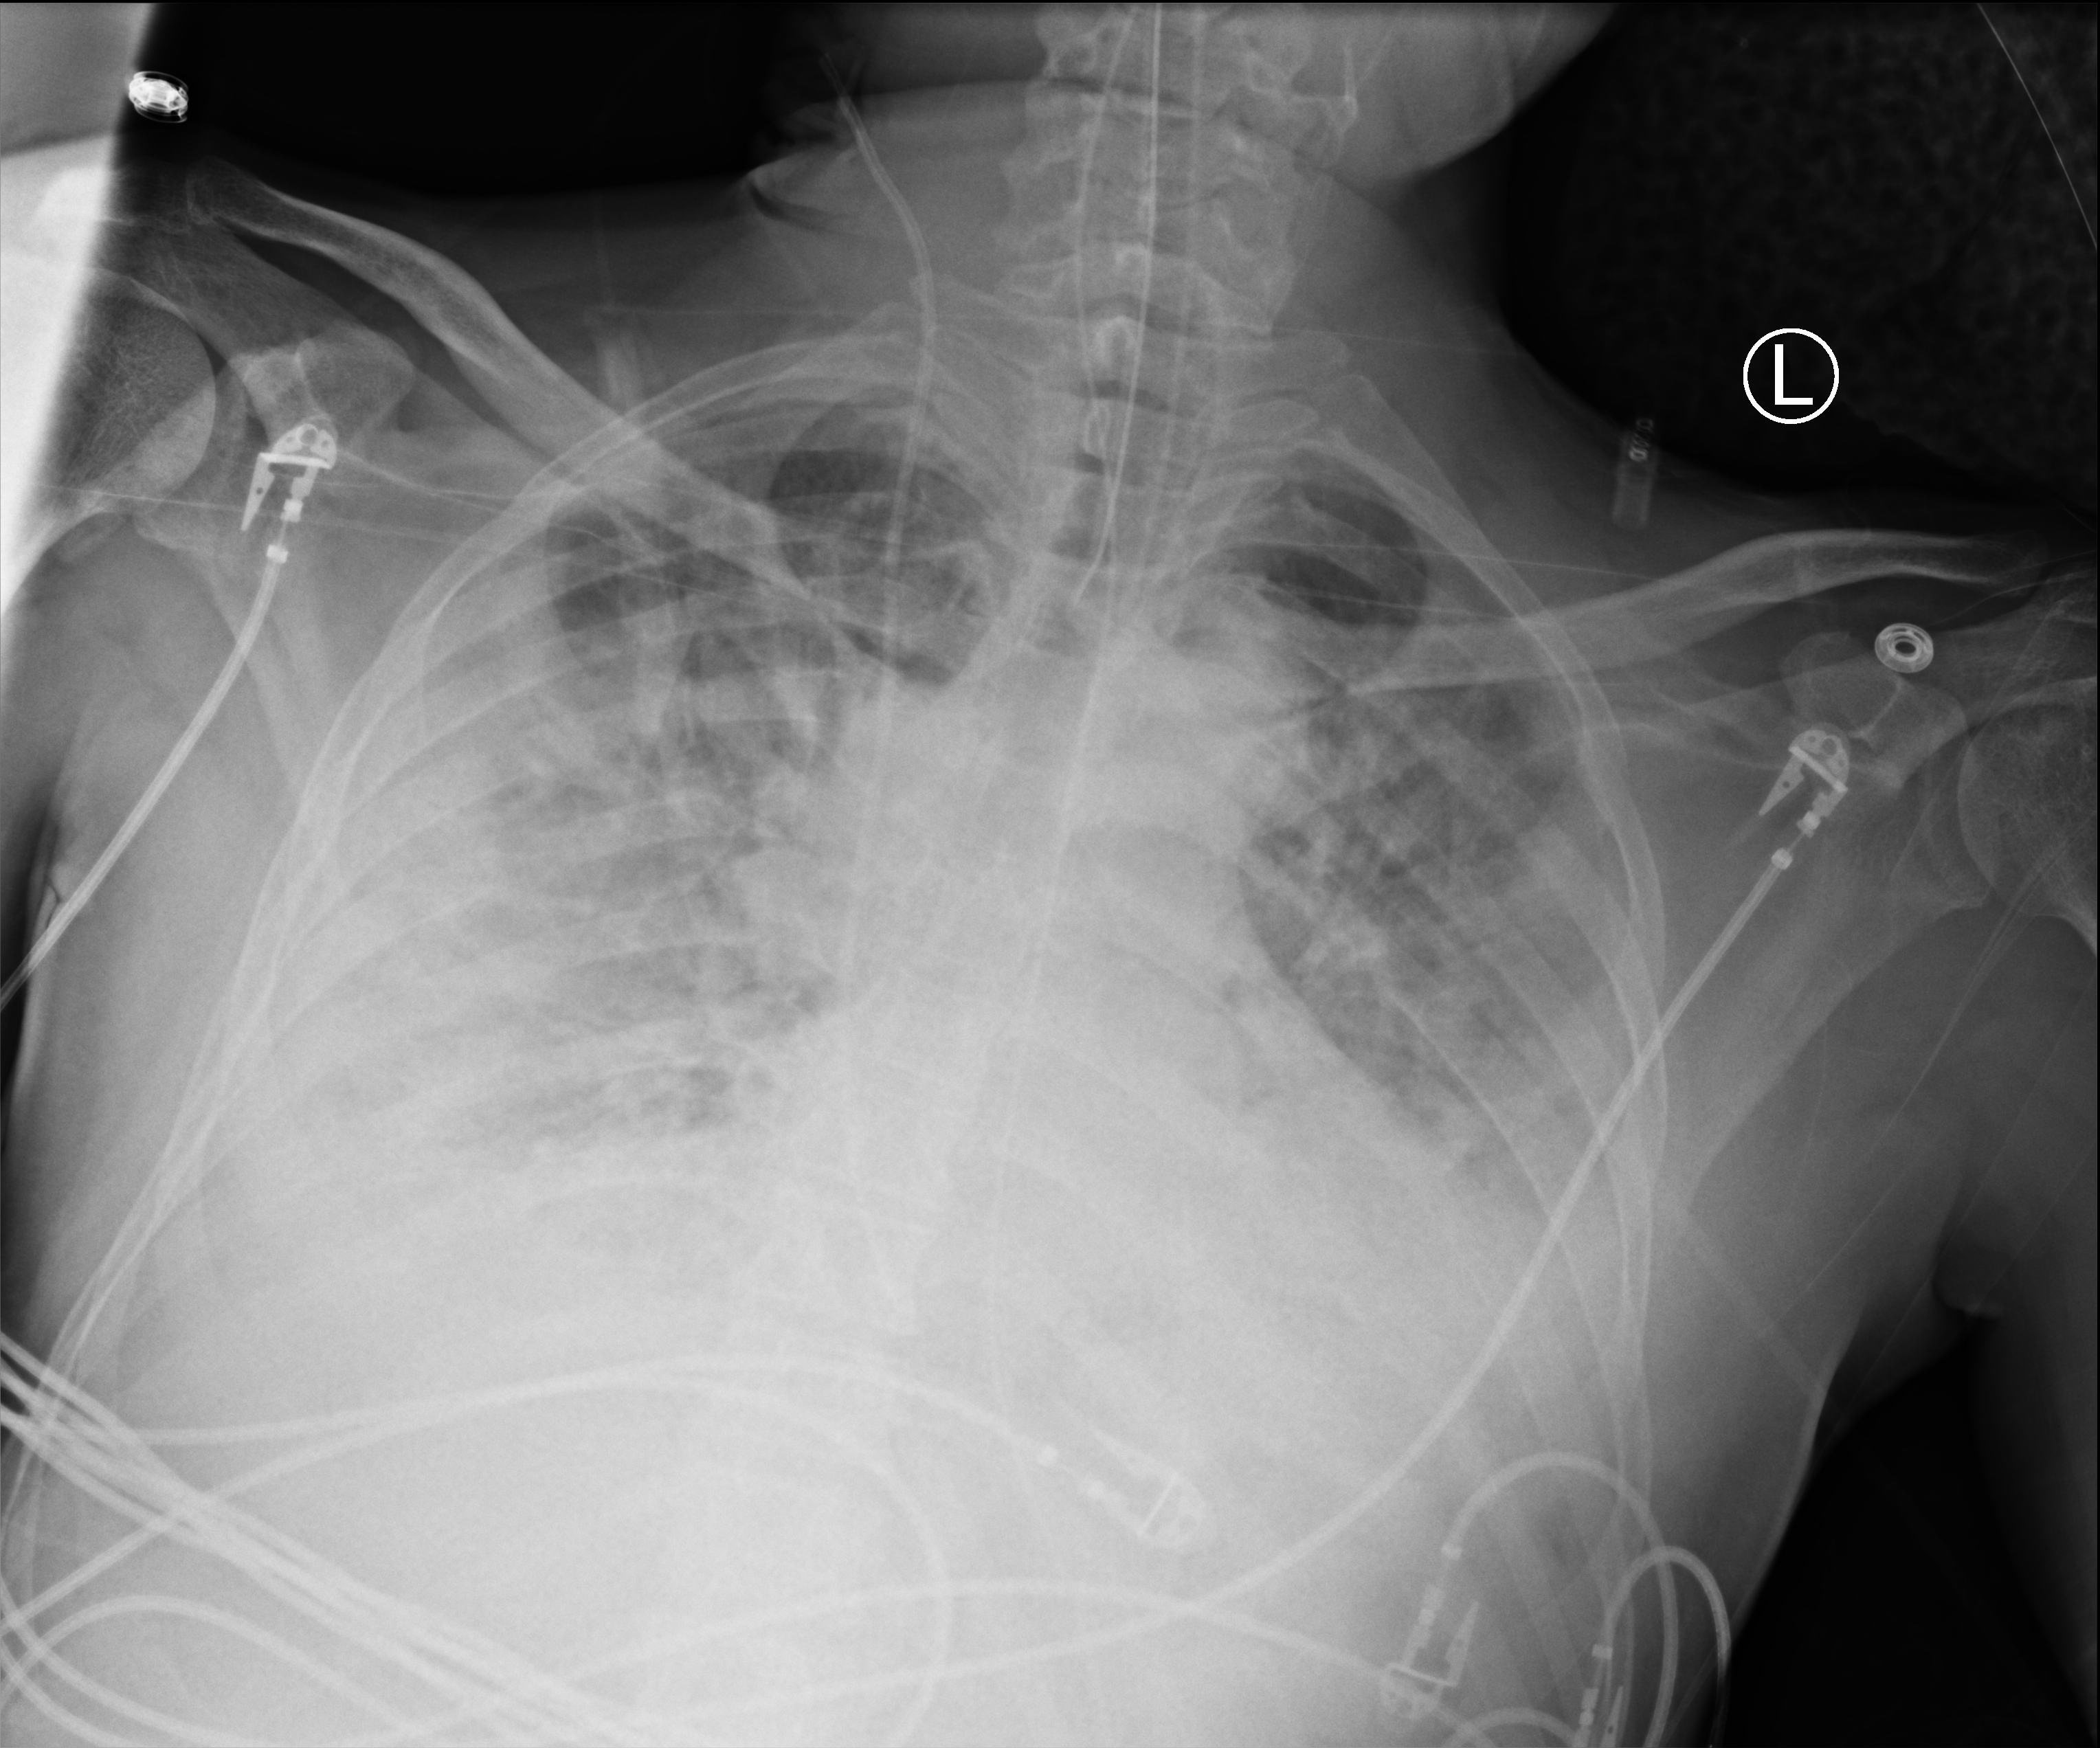
Bedside chest radiograph (computed radiography); anteroposterior (AP) projection. Patient hospitalised with COVID-19; male, aged 18–59 years.
Hospital-stay facts (about this admission, not read from this image; timing relative to this image not recorded):
- mechanically ventilated during this hospital stay: yes
- admitted to intensive care during this hospital stay: yes
- chronic kidney disease (admission record): no